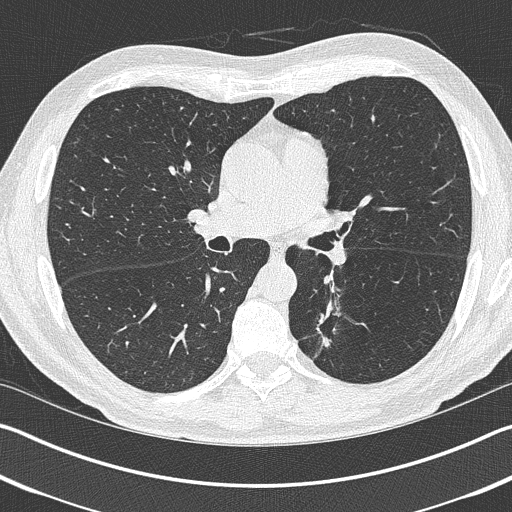
Low-dose screening chest CT, one axial slice. Slice 237 of 402 in the series (ordered by position). Reconstruction kernel B50f. 120 kVp. Lung window (W 1500 / L -600 HU). 1 mm slice thickness. 512 × 512 image matrix, field of view 340 × 340 mm.
Outlined on this slice (manually delineated by an expert):
- lesion 1 (tumor, lower lobe of left lung): bounding box (x1, y1, x2, y2) in pixels: (316, 314, 331, 347)